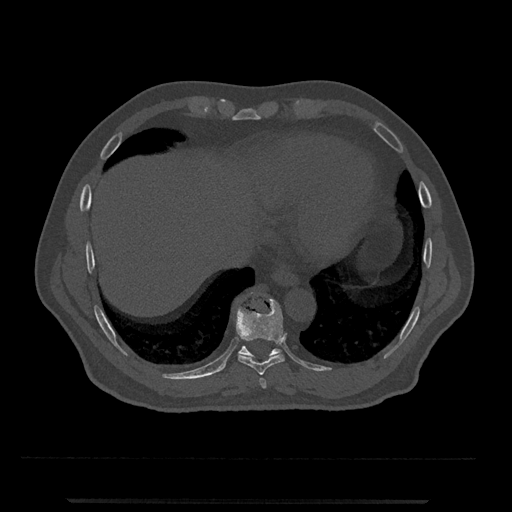
CT including the spine, one axial slice. Position 556 of 797 along the scan axis. Reconstruction kernel Br40s/3. 120 kVp. Bone window (W 1800 / L 400 HU). 0.5 mm slice thickness. 512 × 512 image matrix, field of view 419 × 419 mm. Male patient, age 63 years. Case-level facts recorded for this patient, not image findings: primary cancer: prostate.
Structures marked on this image (semi-automatically segmented with operator editing):
- T10 vertebra: bounding box (x1, y1, x2, y2) in pixels: (238, 345, 282, 358)
- T8 vertebra: (259, 378, 267, 389)
- T9 vertebra: (236, 299, 285, 375)